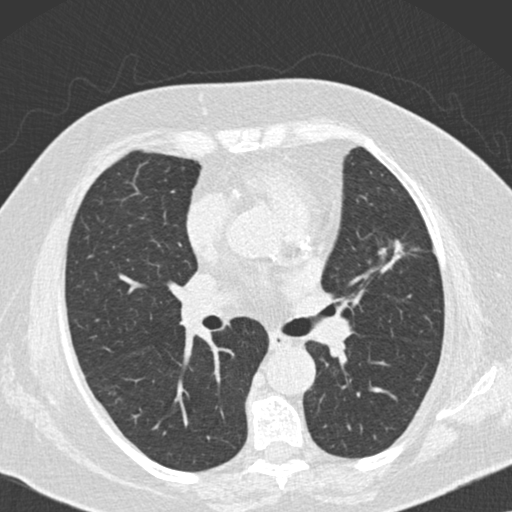
Axial slice from a low-dose chest CT screening exam, baseline screening round, lung window (W 1500 / L -600 HU), 2 mm slice thickness, standard (soft-tissue) reconstruction kernel (B30f), 120 kVp, slice 62 of 160 in the series, 512 × 512 image matrix. Female, age 73 years at enrolment. Current smoker at enrolment.
Expert-annotated lung lesion, bounding box (x1, y1, x2, y2) in pixels: (370, 233, 416, 276). The exam's reader record, not a measurement of the box and not confirmed to be the same lesion: non-calcified nodule or mass ≥4 mm, right lower lobe, 7 × 7 mm, soft tissue attenuation. Note: the box lies in the patient's left hemithorax on this image, whereas the reader's record names the right lung; they may be different findings. Later outcome: lung cancer diagnosed 504 days after this screen (after the second annual screen) — adenocarcinoma, NOS, left upper lobe, moderately differentiated (G2), stage IIIB (AJCC 6th edition), 12 mm at pathology.